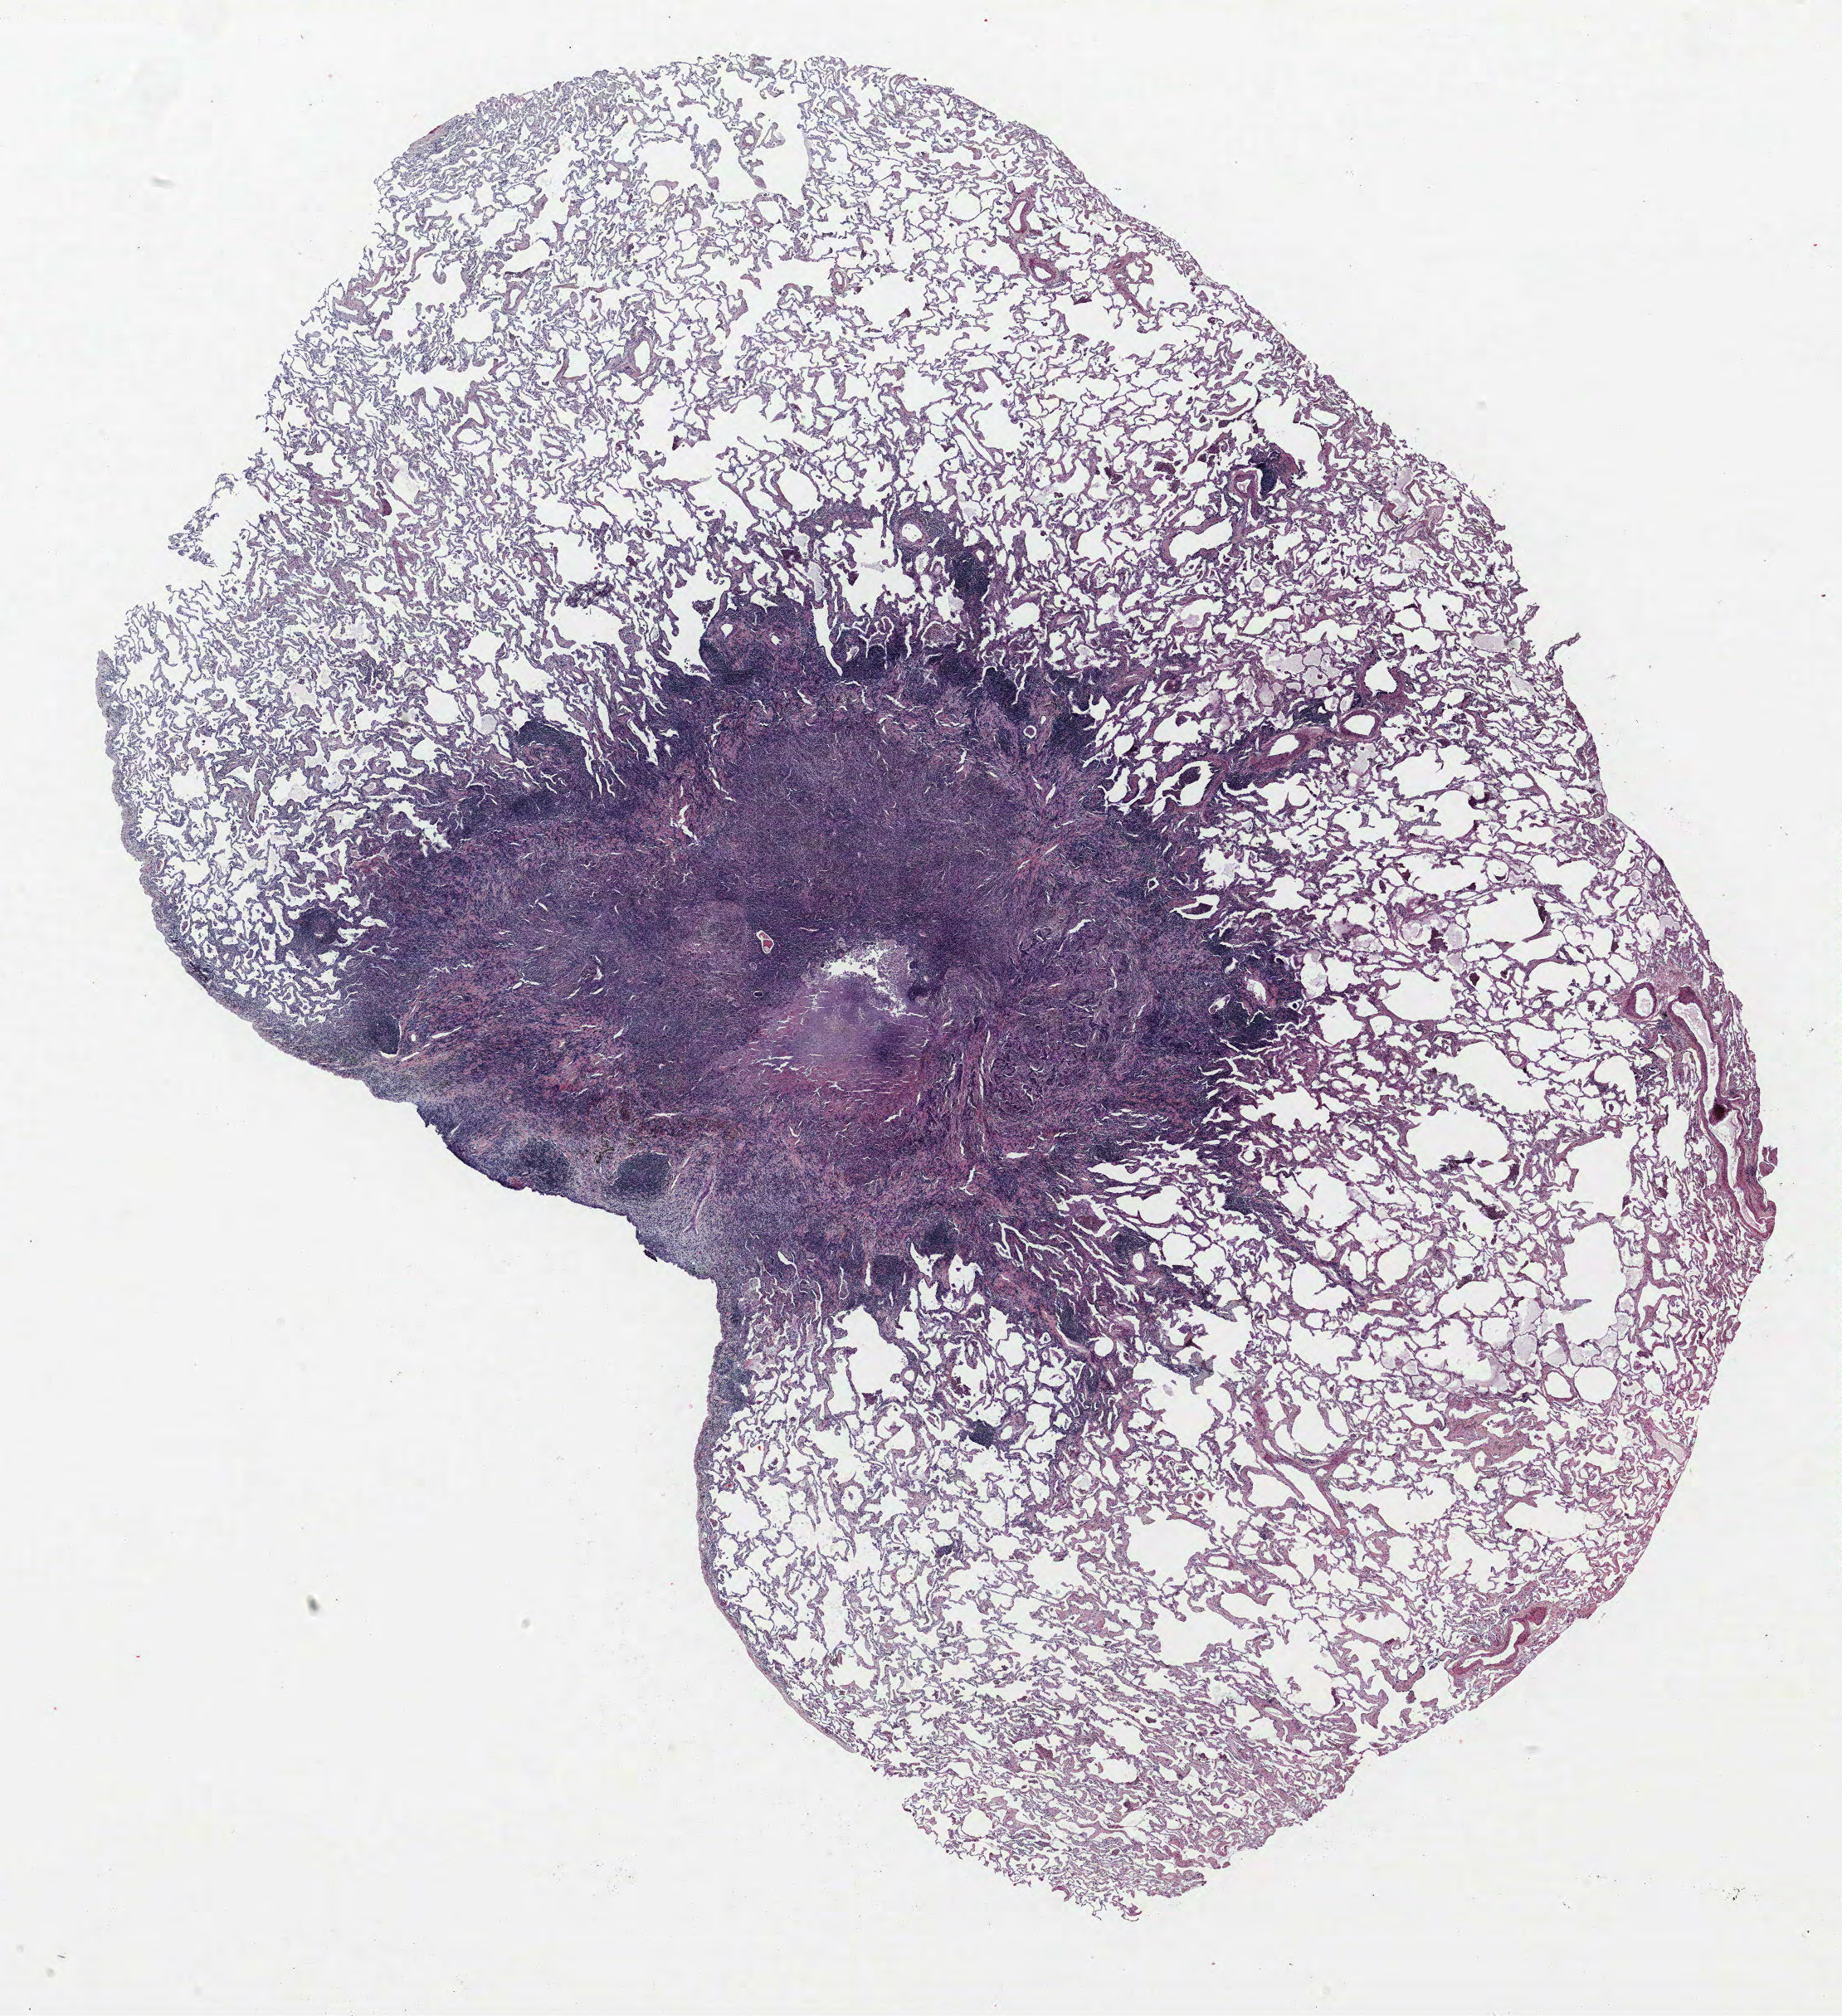
Whole-slide histology image, H&E, low-resolution overview of the scanned area, about 17.8 x 19.4 mm (slide scanned at 40x). Formalin-fixed paraffin-embedded (FFPE) section. Lung tissue. Female, age 55 at enrolment. Current smoker at enrolment. Grade: poorly differentiated (G3).
Participant's lung-cancer diagnosis: Squamous cell carcinoma, NOS (ICD-O-3 8070/3). Stage (AJCC 6th edition): IA. Primary tumour location (clinical record): right upper lobe. Tumour size (pathology): 8 mm.